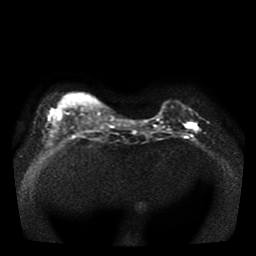
Breast MRI, one axial slice; slice 11 of 41 in the series (ordered by position); diffusion-weighted series; image 2 of 4 stored at this slice position (different b-values; order by instance number); 1.5 T; 256 × 256 image matrix. Female patient.
Outlined on this slice (manually delineated by an expert):
- tumour on diffusion-weighted imaging: bounding box [x1, y1, x2, y2] px = [187, 123, 196, 128]